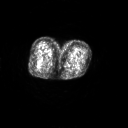
FDG PET of an extremity soft-tissue mass (from a PET/CT study), one axial slice; slice 22 of 267 in the series (ordered by position); 3.27 mm slice thickness; 128 × 128 image matrix, field of view 700 × 700 mm. Patient: female, 70 years. From the clinical record (not read from this slice): histological type: synovial sarcoma; grade: intermediate; site of the primary tumour: right buttock.
Outlined on this slice (expert contour drawn on MRI and transferred to this co-registered scan by the dataset authors):
- gross tumour volume including surrounding oedema: bounding box (x1, y1, x2, y2) in pixels: (34, 61, 39, 68)